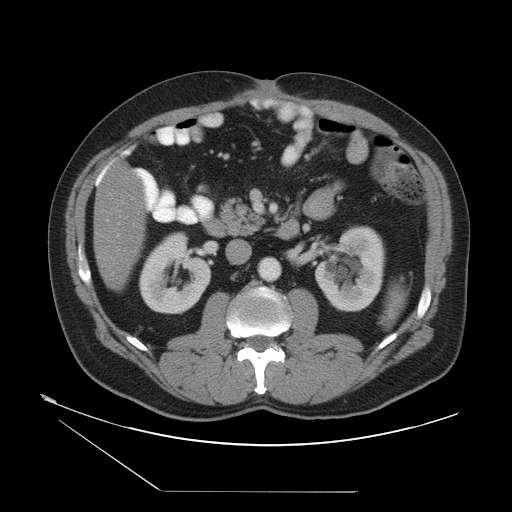
Contrast-enhanced abdominal CT, one axial slice. Position 17 of 55 along the scan axis. Intravenous contrast given. Soft-tissue window (W 400 / L 40 HU). 512 × 512 image matrix. Male patient, age 59 years. From the clinical record (not read from this slice): diagnosis: colorectal cancer liver metastases, imaged before liver resection; multiple liver metastases: yes; largest metastasis: 0.3 cm.
Annotated regions visible in this slice (expert manual segmentation):
- hepatic veins: bounding box (x1, y1, x2, y2) in pixels: (117, 218, 126, 225)
- liver: (95, 164, 145, 288)
- planned liver remnant (the part of the liver to remain after resection): (95, 164, 145, 289)
- portal vein (with intrahepatic branches): (116, 202, 122, 237)